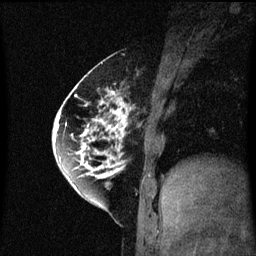
Breast MRI (dynamic contrast-enhanced), one sagittal slice; slice 22 of 60 in the series (ordered by position); dynamic contrast-enhanced series, image 2 of 3 at this slice position (ordered by acquisition); 1.5 T; TE 4.2 ms, TR 8.4 ms; 256 × 256 image matrix, field of view 200 × 200 mm. Female patient, age 60 years.
Annotated regions visible in this slice (semi-automatic segmentation, software-assisted and operator-edited):
- analysis volume of interest (the breast-tissue region the enhancement analysis was run in; not a lesion): bounding box <64,70,133,195> (left, top, right, bottom; pixels)
- tumour enhancement mask (voxels above the 70 % enhancement threshold inside the analysis volume of interest): <64,70,131,189>